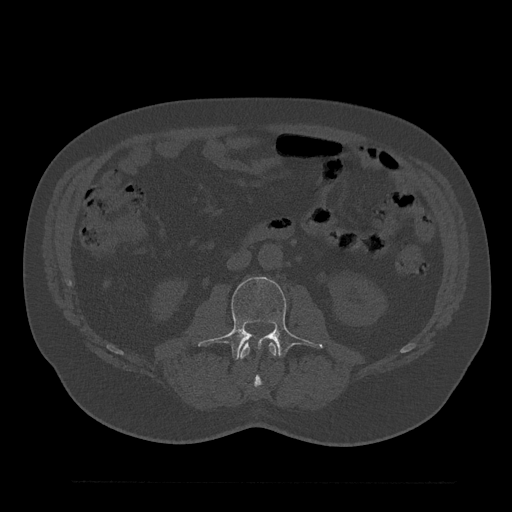
CT including the spine, one axial slice; reconstruction kernel Br40s/3; 120 kVp; bone window (W 1800 / L 400 HU); 0.5 mm slice thickness; 512 × 512 image matrix, field of view 430 × 430 mm. Patient: male, 61 years. Case-level facts recorded for this patient, not image findings: primary cancer: prostate.
Structures marked on this image (semi-automatically segmented with operator editing):
- L2 vertebra: bounding box [x1, y1, x2, y2] px = [238, 342, 277, 396]
- L3 vertebra: [198, 277, 323, 360]